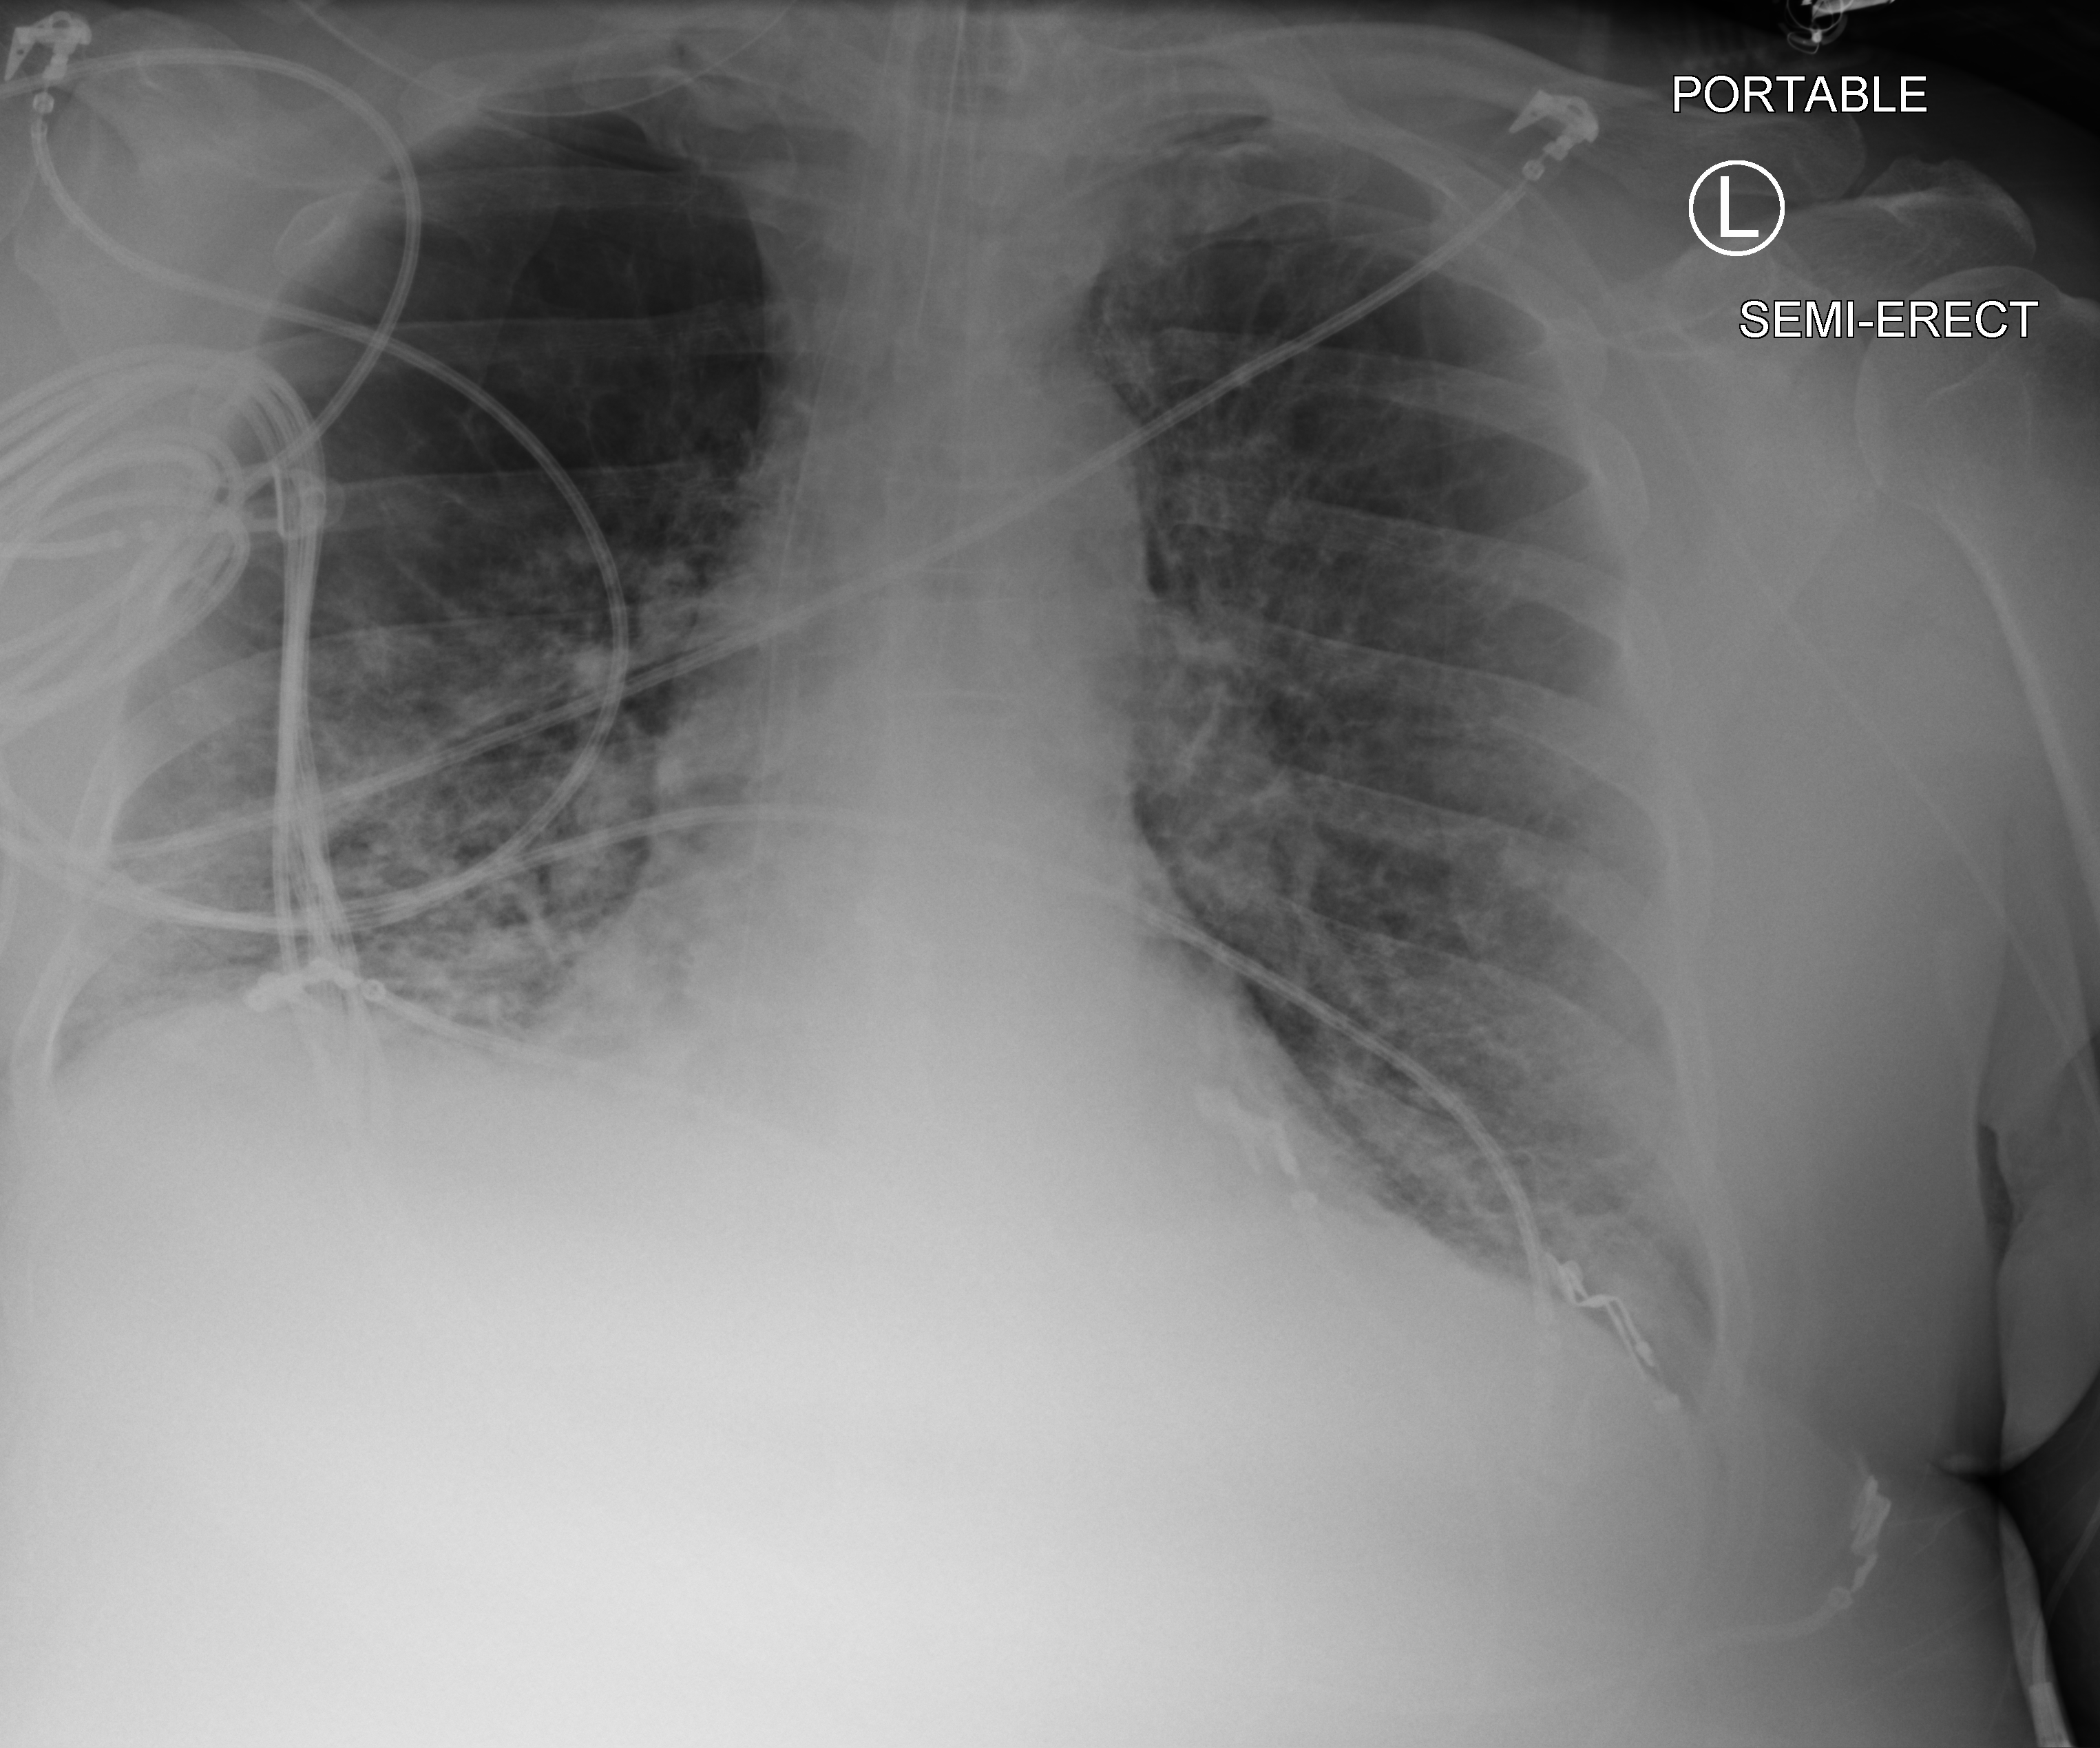
Chest X-ray (portable), anteroposterior (AP) projection. Adult patient hospitalised with COVID-19, age 18–59 years.
Admission-level facts for this patient (not findings on this image; timing relative to this image not recorded):
- COPD (admission record): yes
- mechanically ventilated during this hospital stay: yes